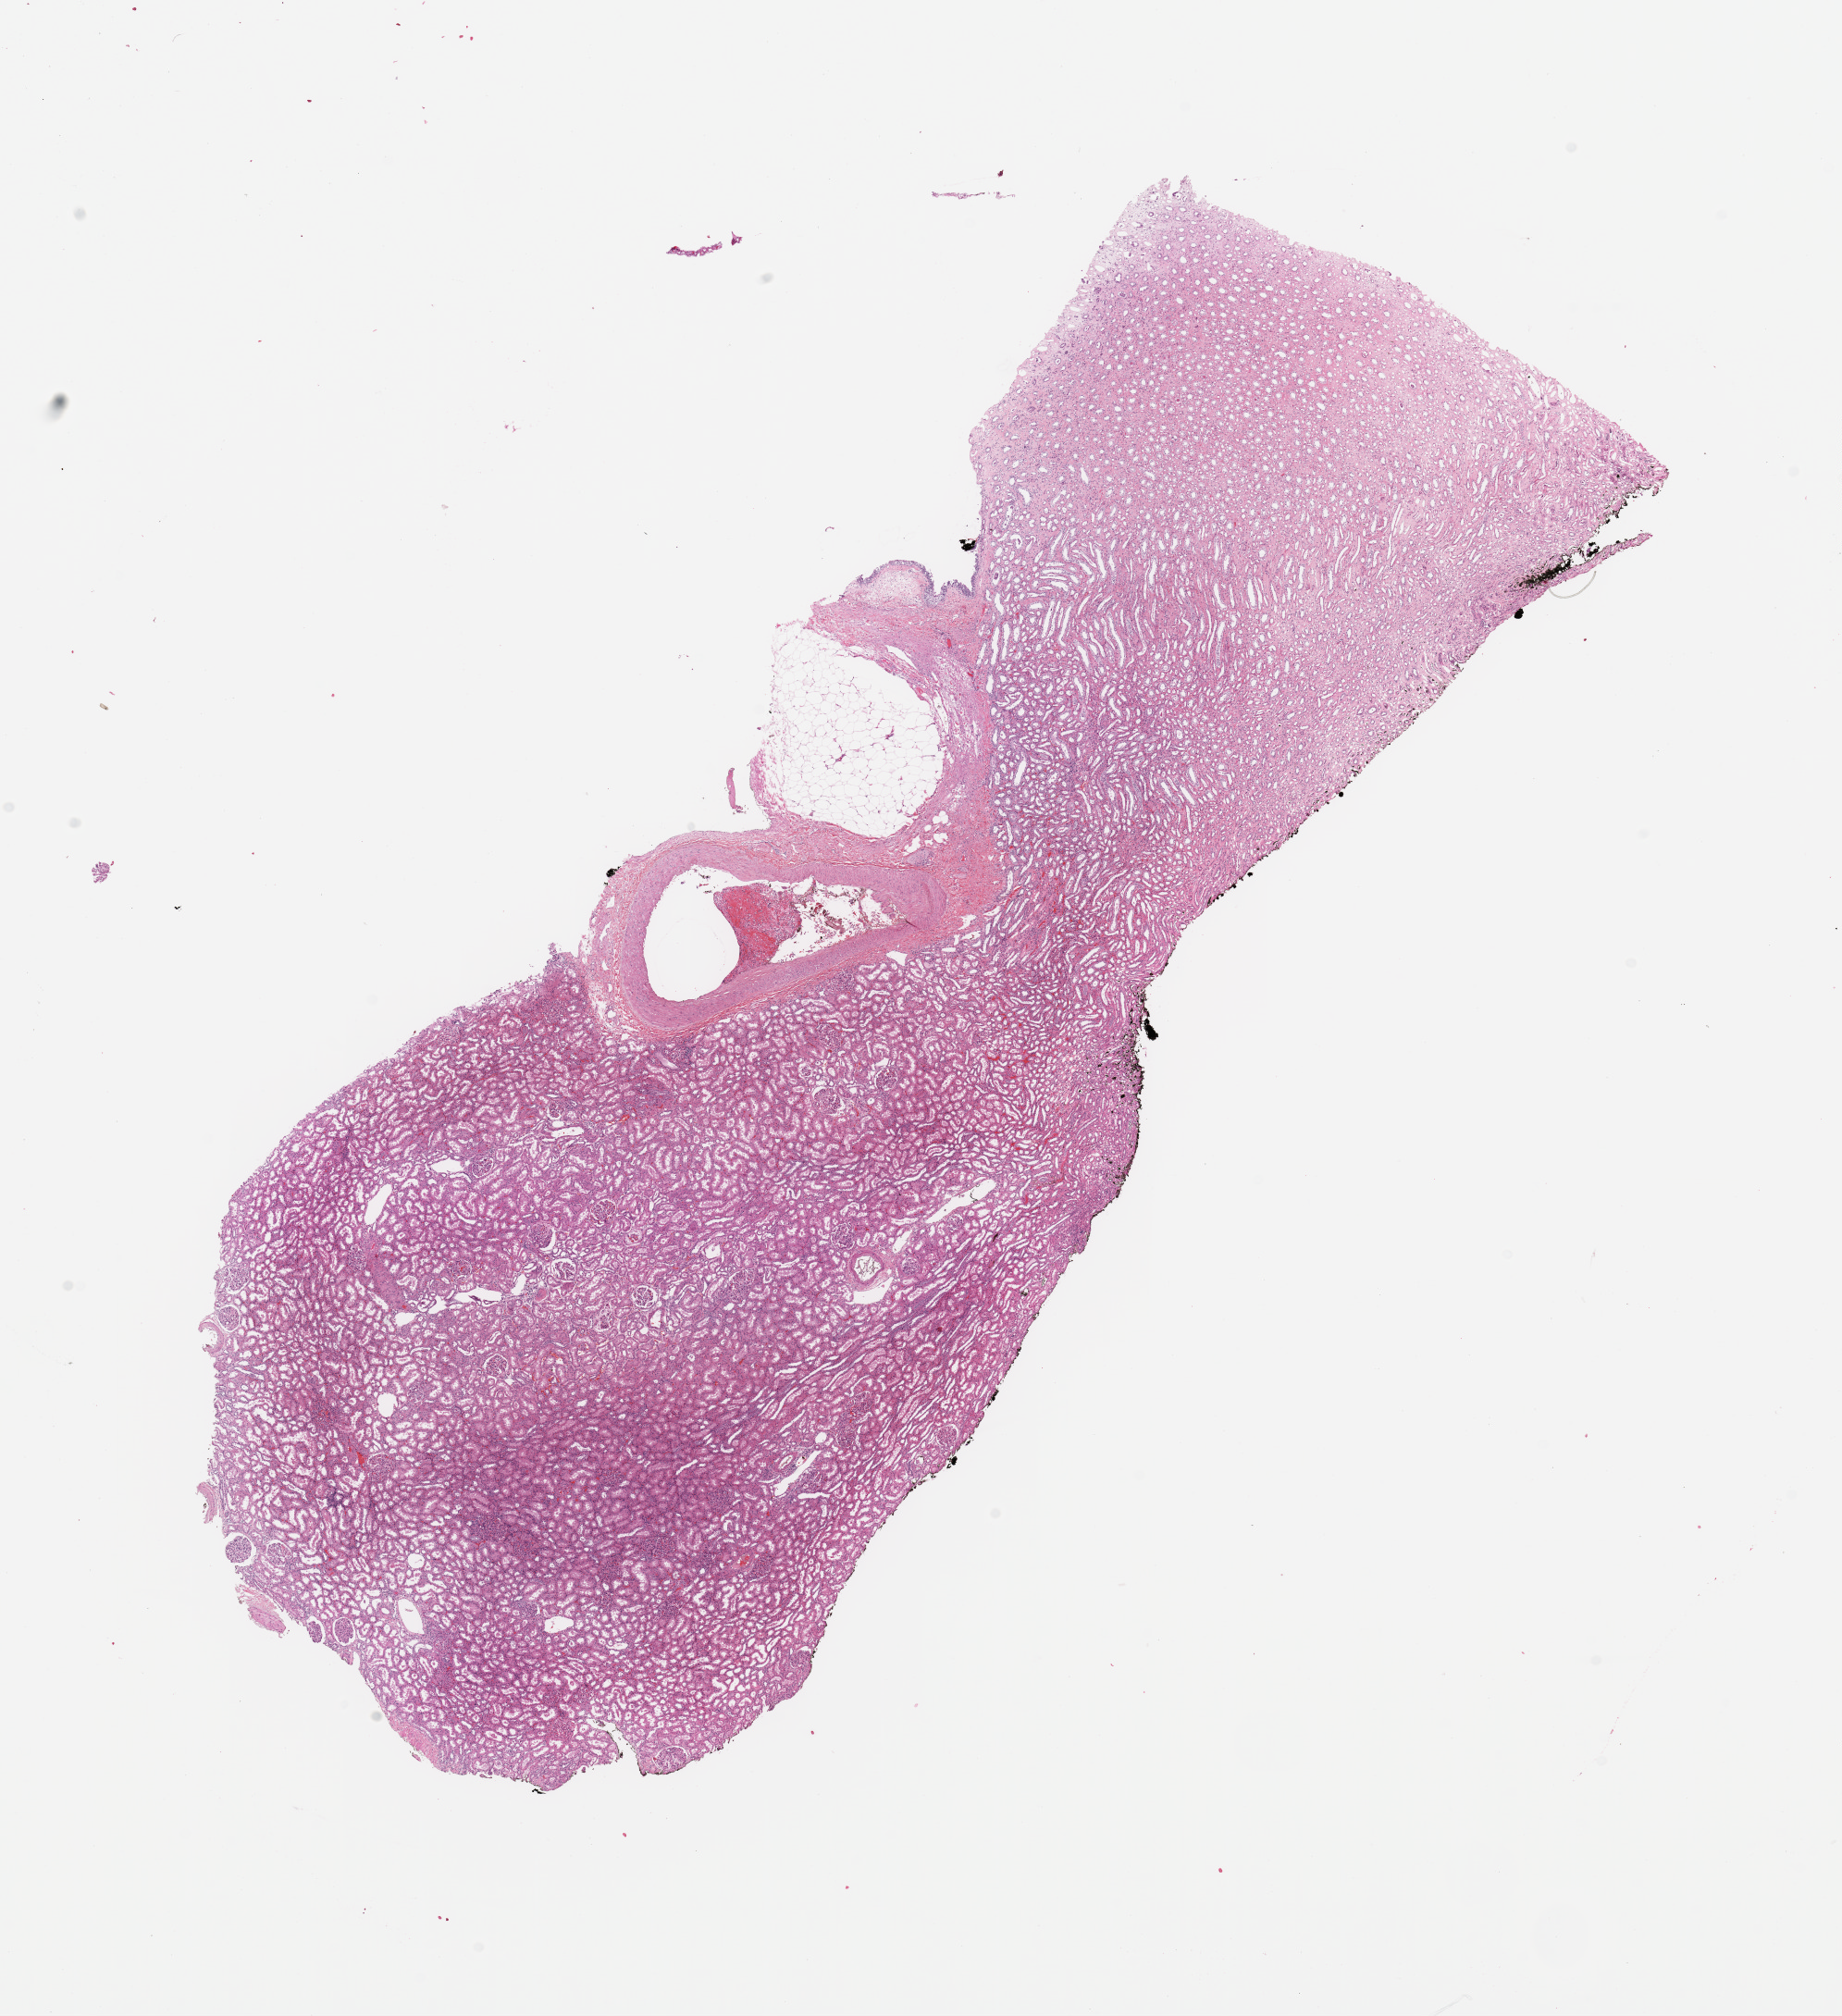
H&E-stained whole-slide image — low-resolution overview of the scanned area, about 15.8 x 17.2 mm. Normal (non-tumour) tissue sample, sampled site: kidney. 51-year-old female patient.
This section: normal (non-tumour) tissue from the same patient. Patient diagnosis: Renal cell carcinoma, NOS.